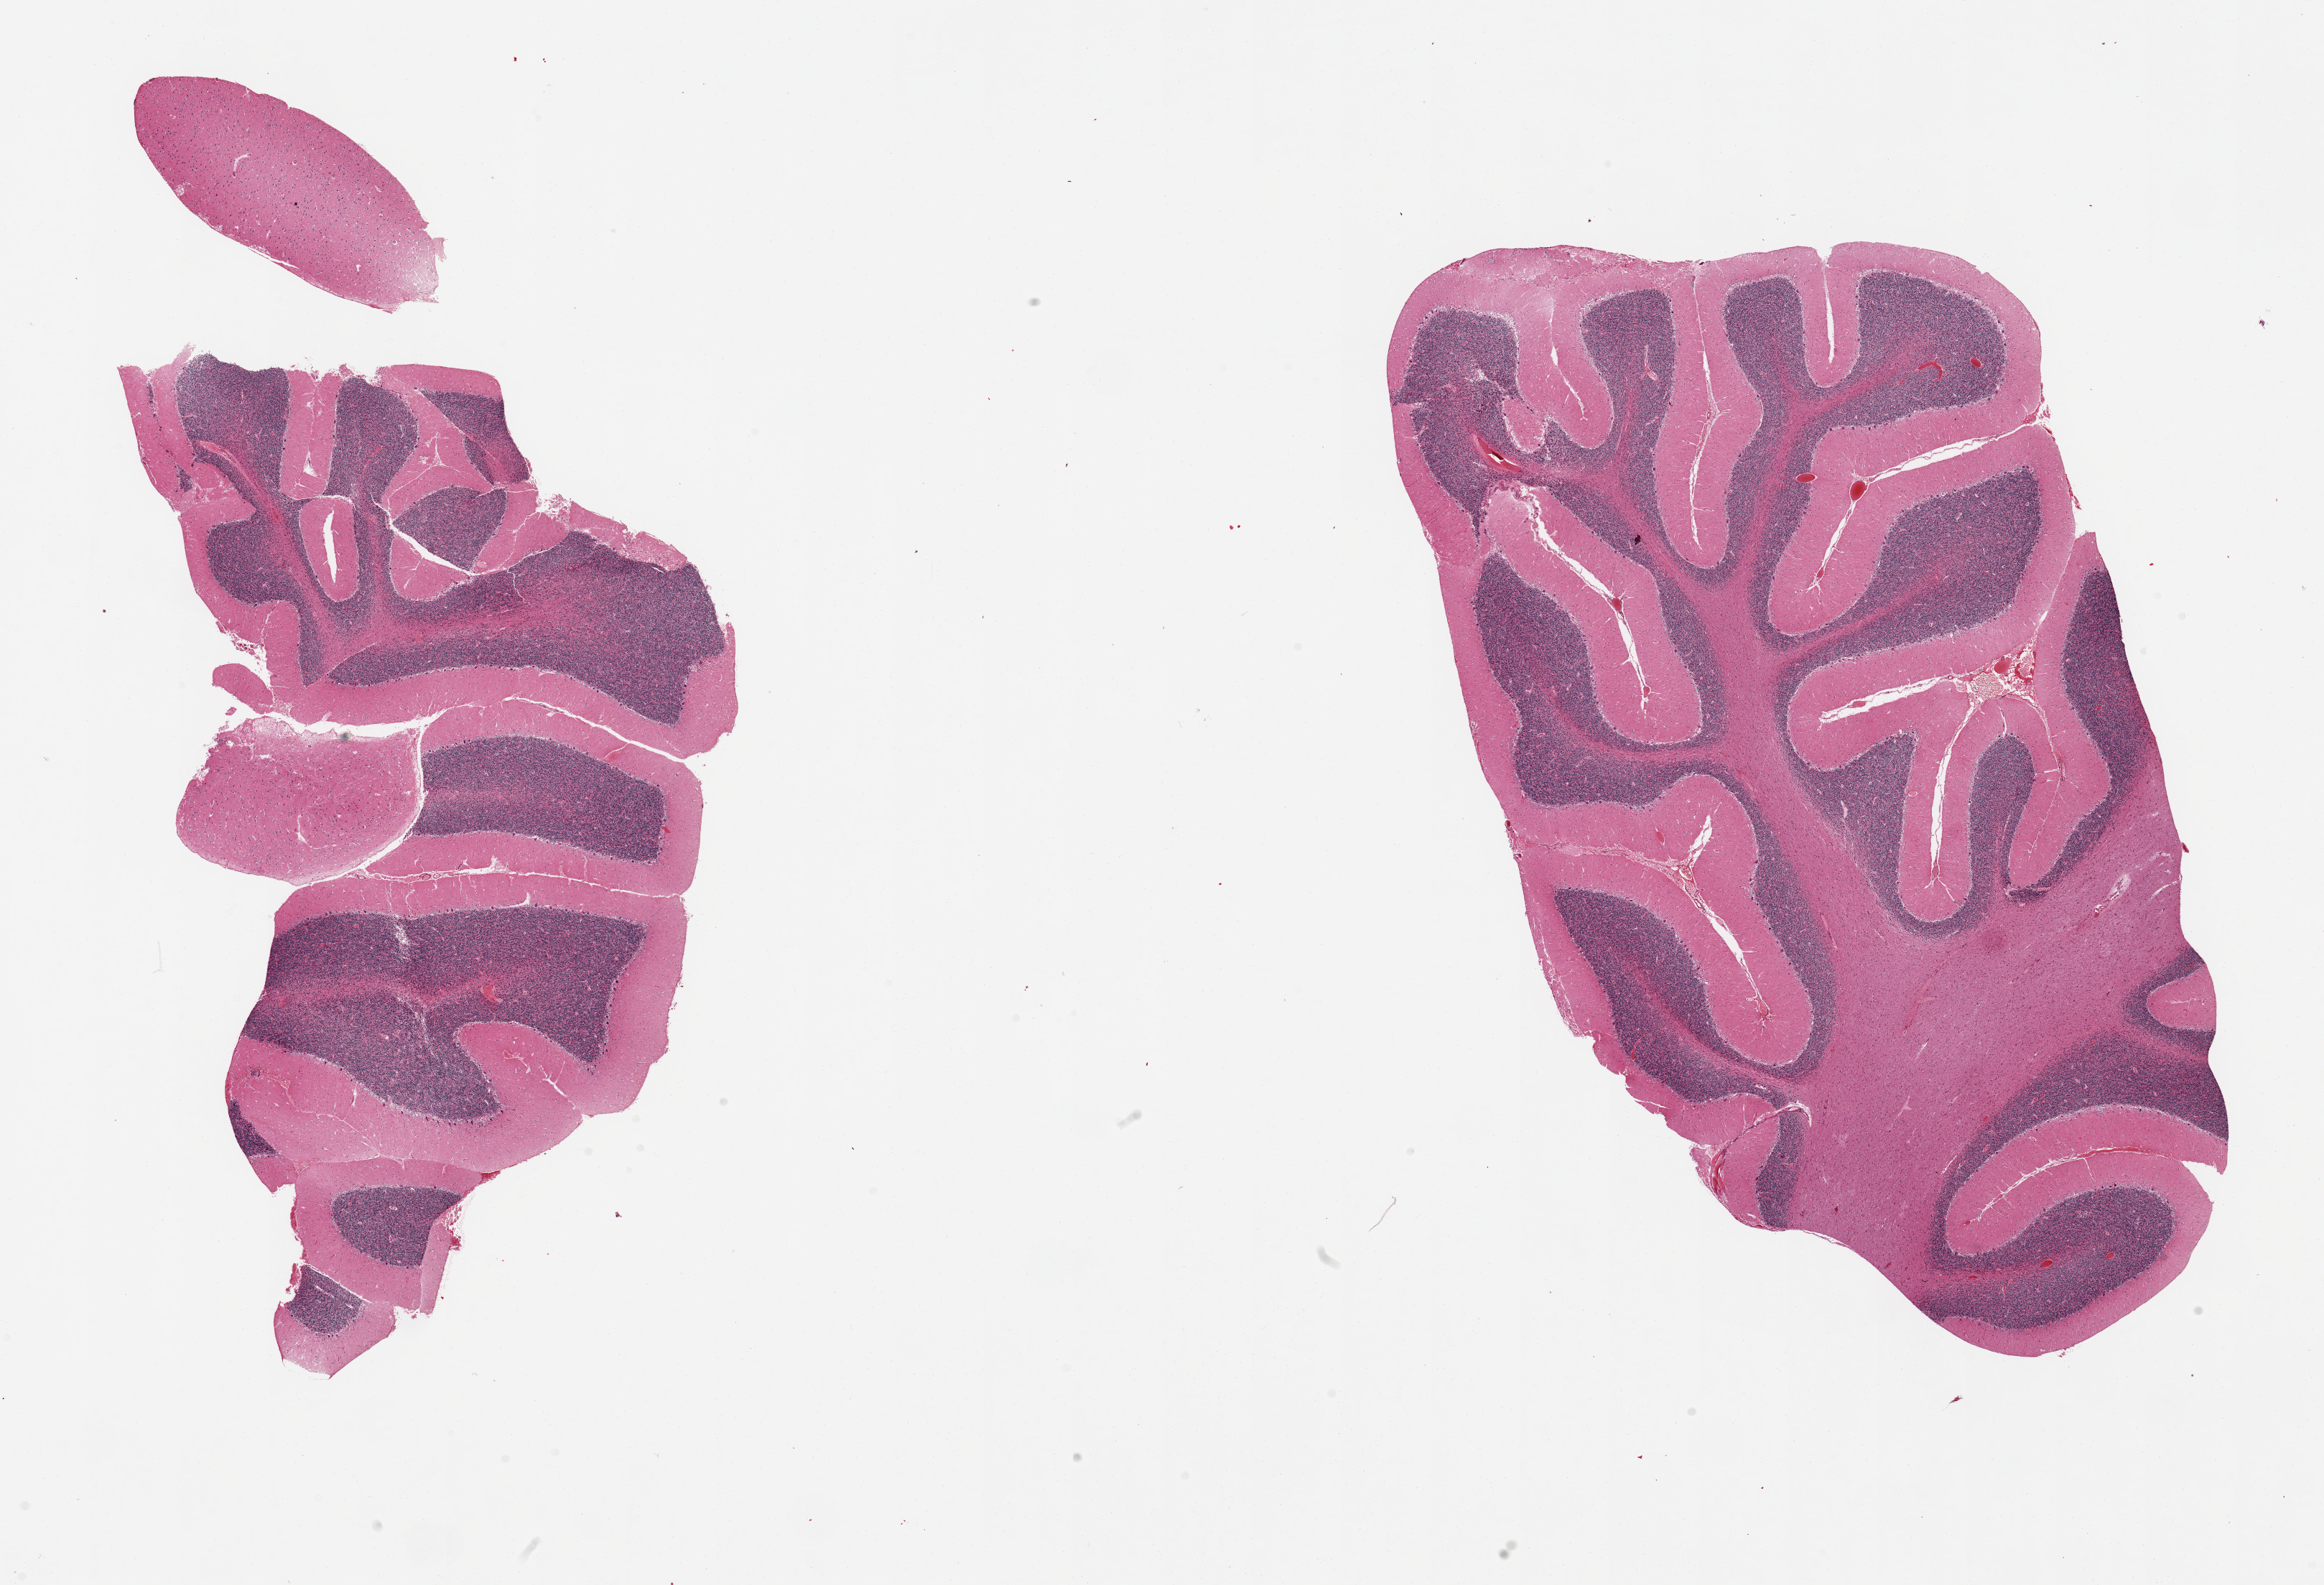
Digitized hematoxylin and eosin (H&E)-stained section, brightfield — a low-resolution overview of the entire scanned area, about 25.6 x 17.5 mm (from a 20x scan); PAXgene-fixed paraffin-embedded (PFPE) section; sampled site (target tissue): cerebellum; tissue donor sample. Donor: male.
Pathologist's review note for this sample: 2 pieces.